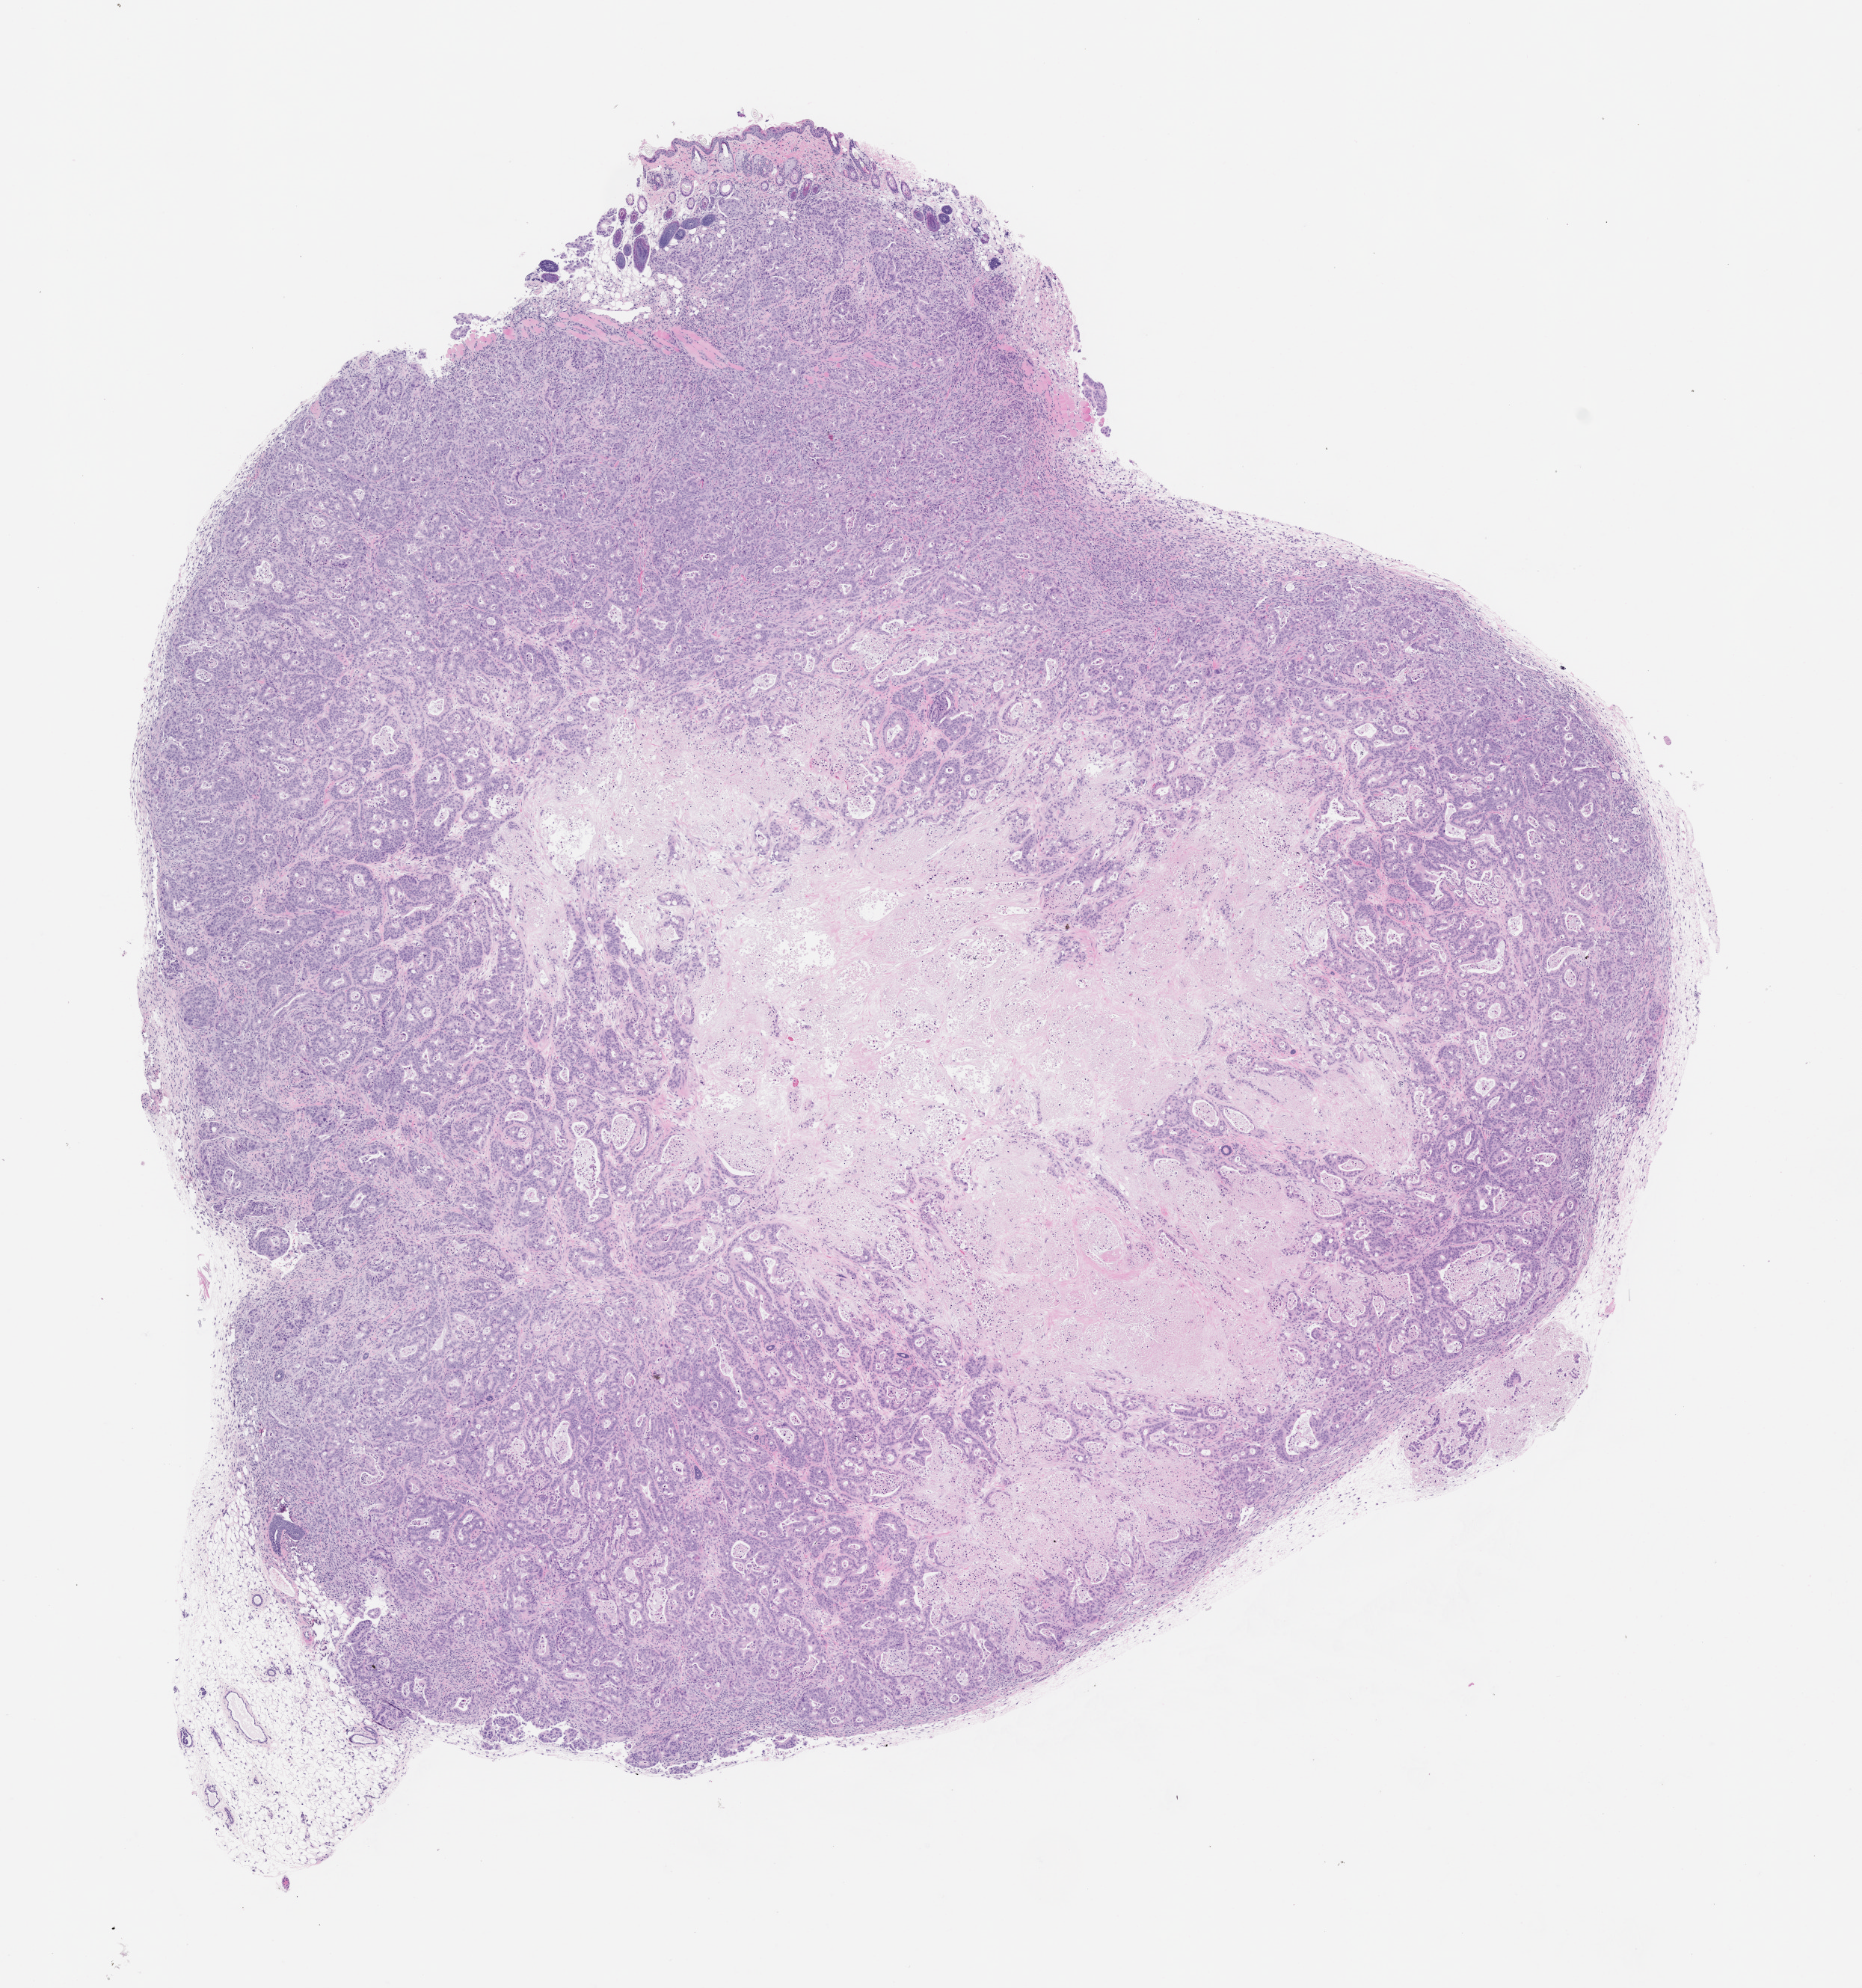
Whole-slide image, hematoxylin and eosin (H&E): patient-derived xenograft (human tumor grown in a mouse), passage 2, a low-resolution overview of the entire scanned area, about 10.0 x 10.7 mm. Formalin-fixed, paraffin-embedded (FFPE) tissue. Tumor site category: pancreas.
Originating patient diagnosis: Pancreatic Adenocarcinoma.